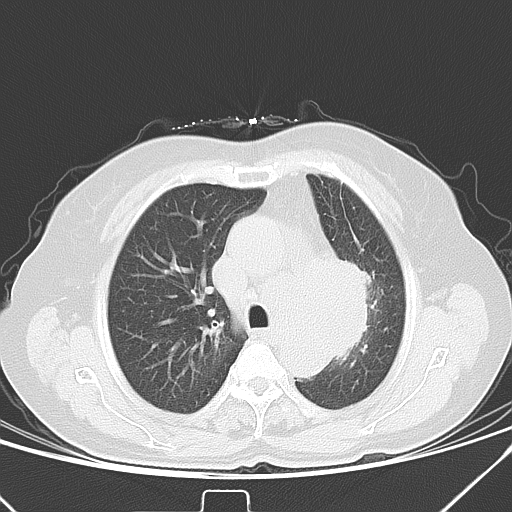
Chest CT, one axial slice. Slice 28 of 40 in the series (ordered by position). 120 kVp. Lung window (W 1500 / L -600 HU). 5 mm slice thickness. 512 × 512 image matrix. Female patient, age 59 years. From the clinical record (not read from this slice): clinical TNM (as recorded): T3 N1 M0; histopathological grade: G3.
Outlined on this slice (bounding box drawn by a radiologist):
- lung tumour (recorded histology: small cell carcinoma): box from (x=335, y=241) to (x=383, y=366) px